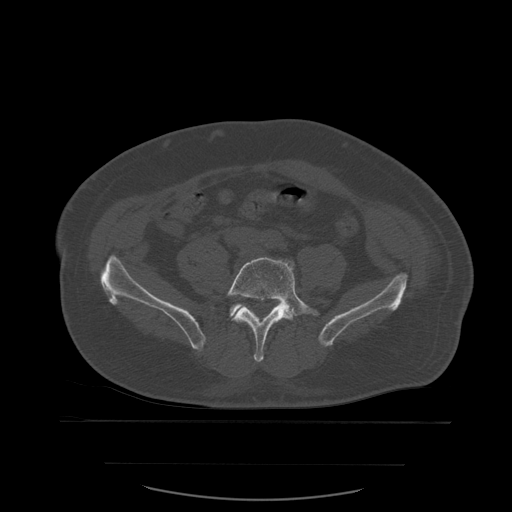
CT including the spine, one axial slice; bone window (W 1800 / L 400 HU); 512 × 512 image matrix, field of view 479 × 479 mm. Patient age 71 years. Case-level facts recorded for this patient, not image findings: primary cancer: lung; vertebrae with lytic lesions (as recorded): T1, T2, L5, S1.
Annotated regions visible in this slice (semi-automatic segmentation, software-assisted and operator-edited):
- L5 vertebra: box from (x=226, y=257) to (x=320, y=362) px